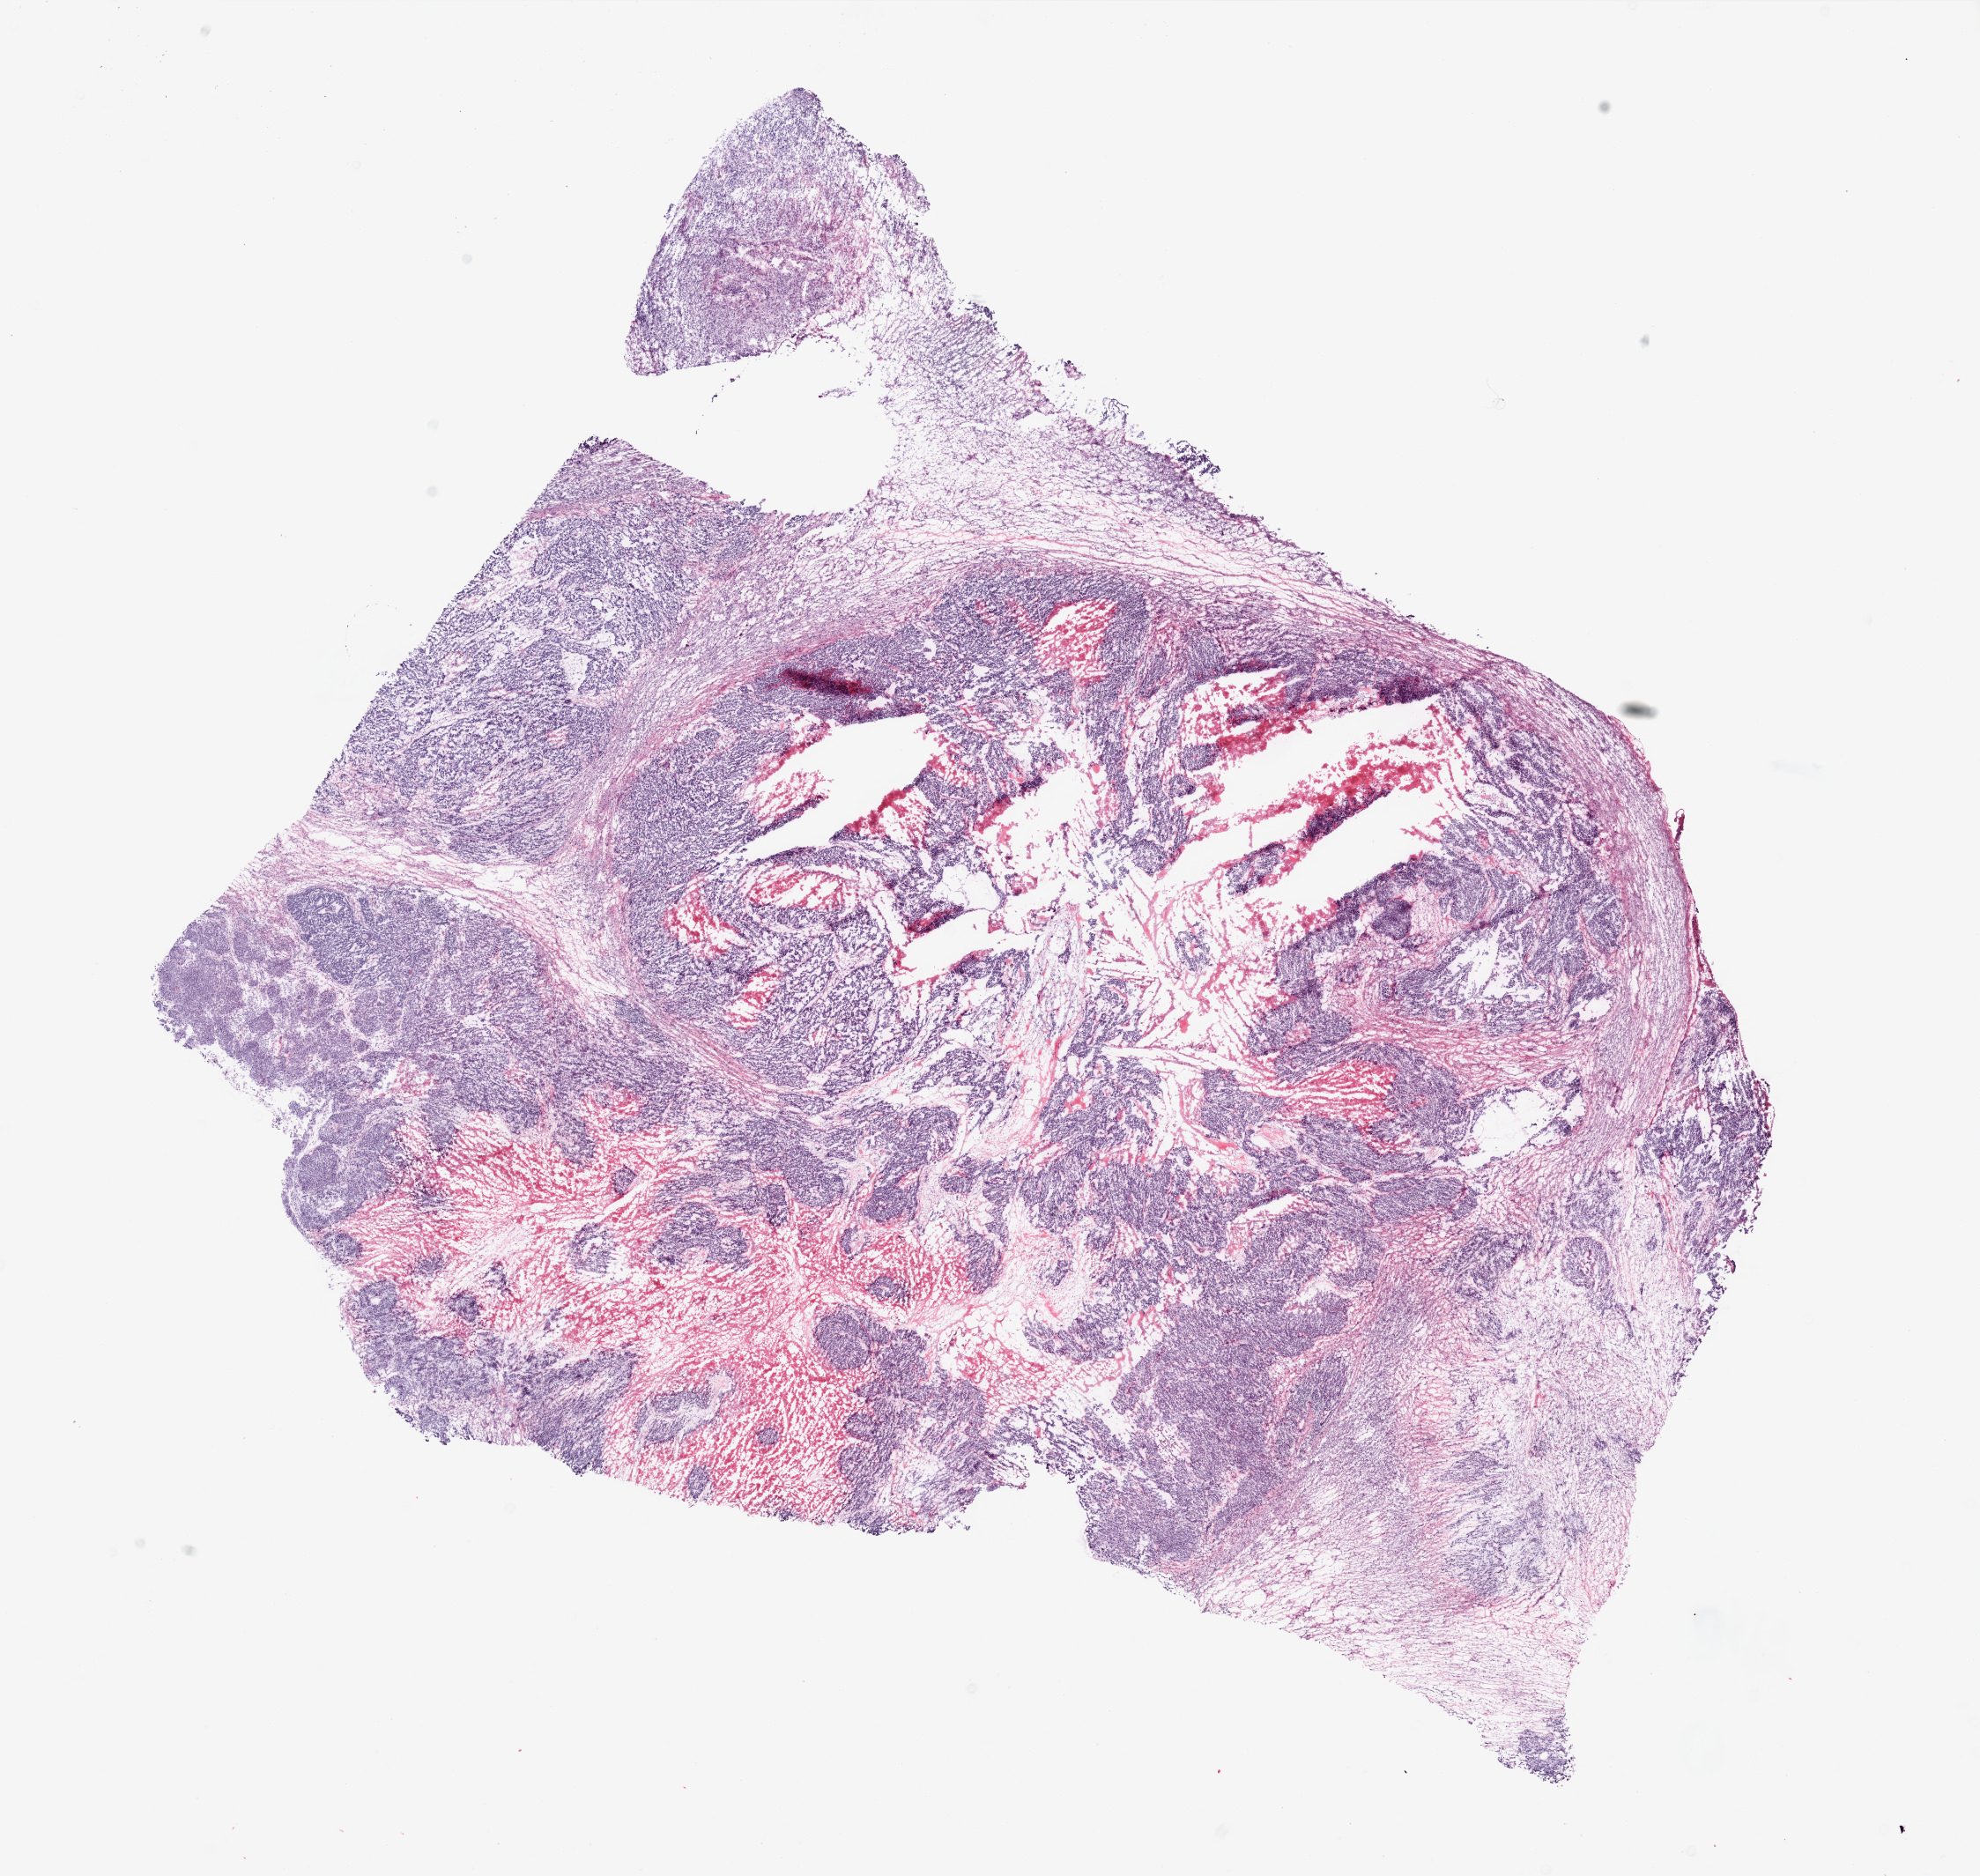
Hematoxylin and eosin (H&E) stained whole-slide image — low-resolution overview of the scanned area, about 18.0 x 17.0 mm (slide scanned at 20x); frozen section from the top of the tissue portion; ovary, primary tumour sample. Female, age 50 years at initial diagnosis. Histologic grade: G3 (poorly differentiated). Slide review estimates, as recorded: tumour cells 50%, tumour nuclei 70%, normal cells 30%, stromal cells 0%, necrosis 20%.
- FIGO stage: IIIC
- pathologic diagnosis: Serous cystadenocarcinoma, NOS
- laterality: bilateral